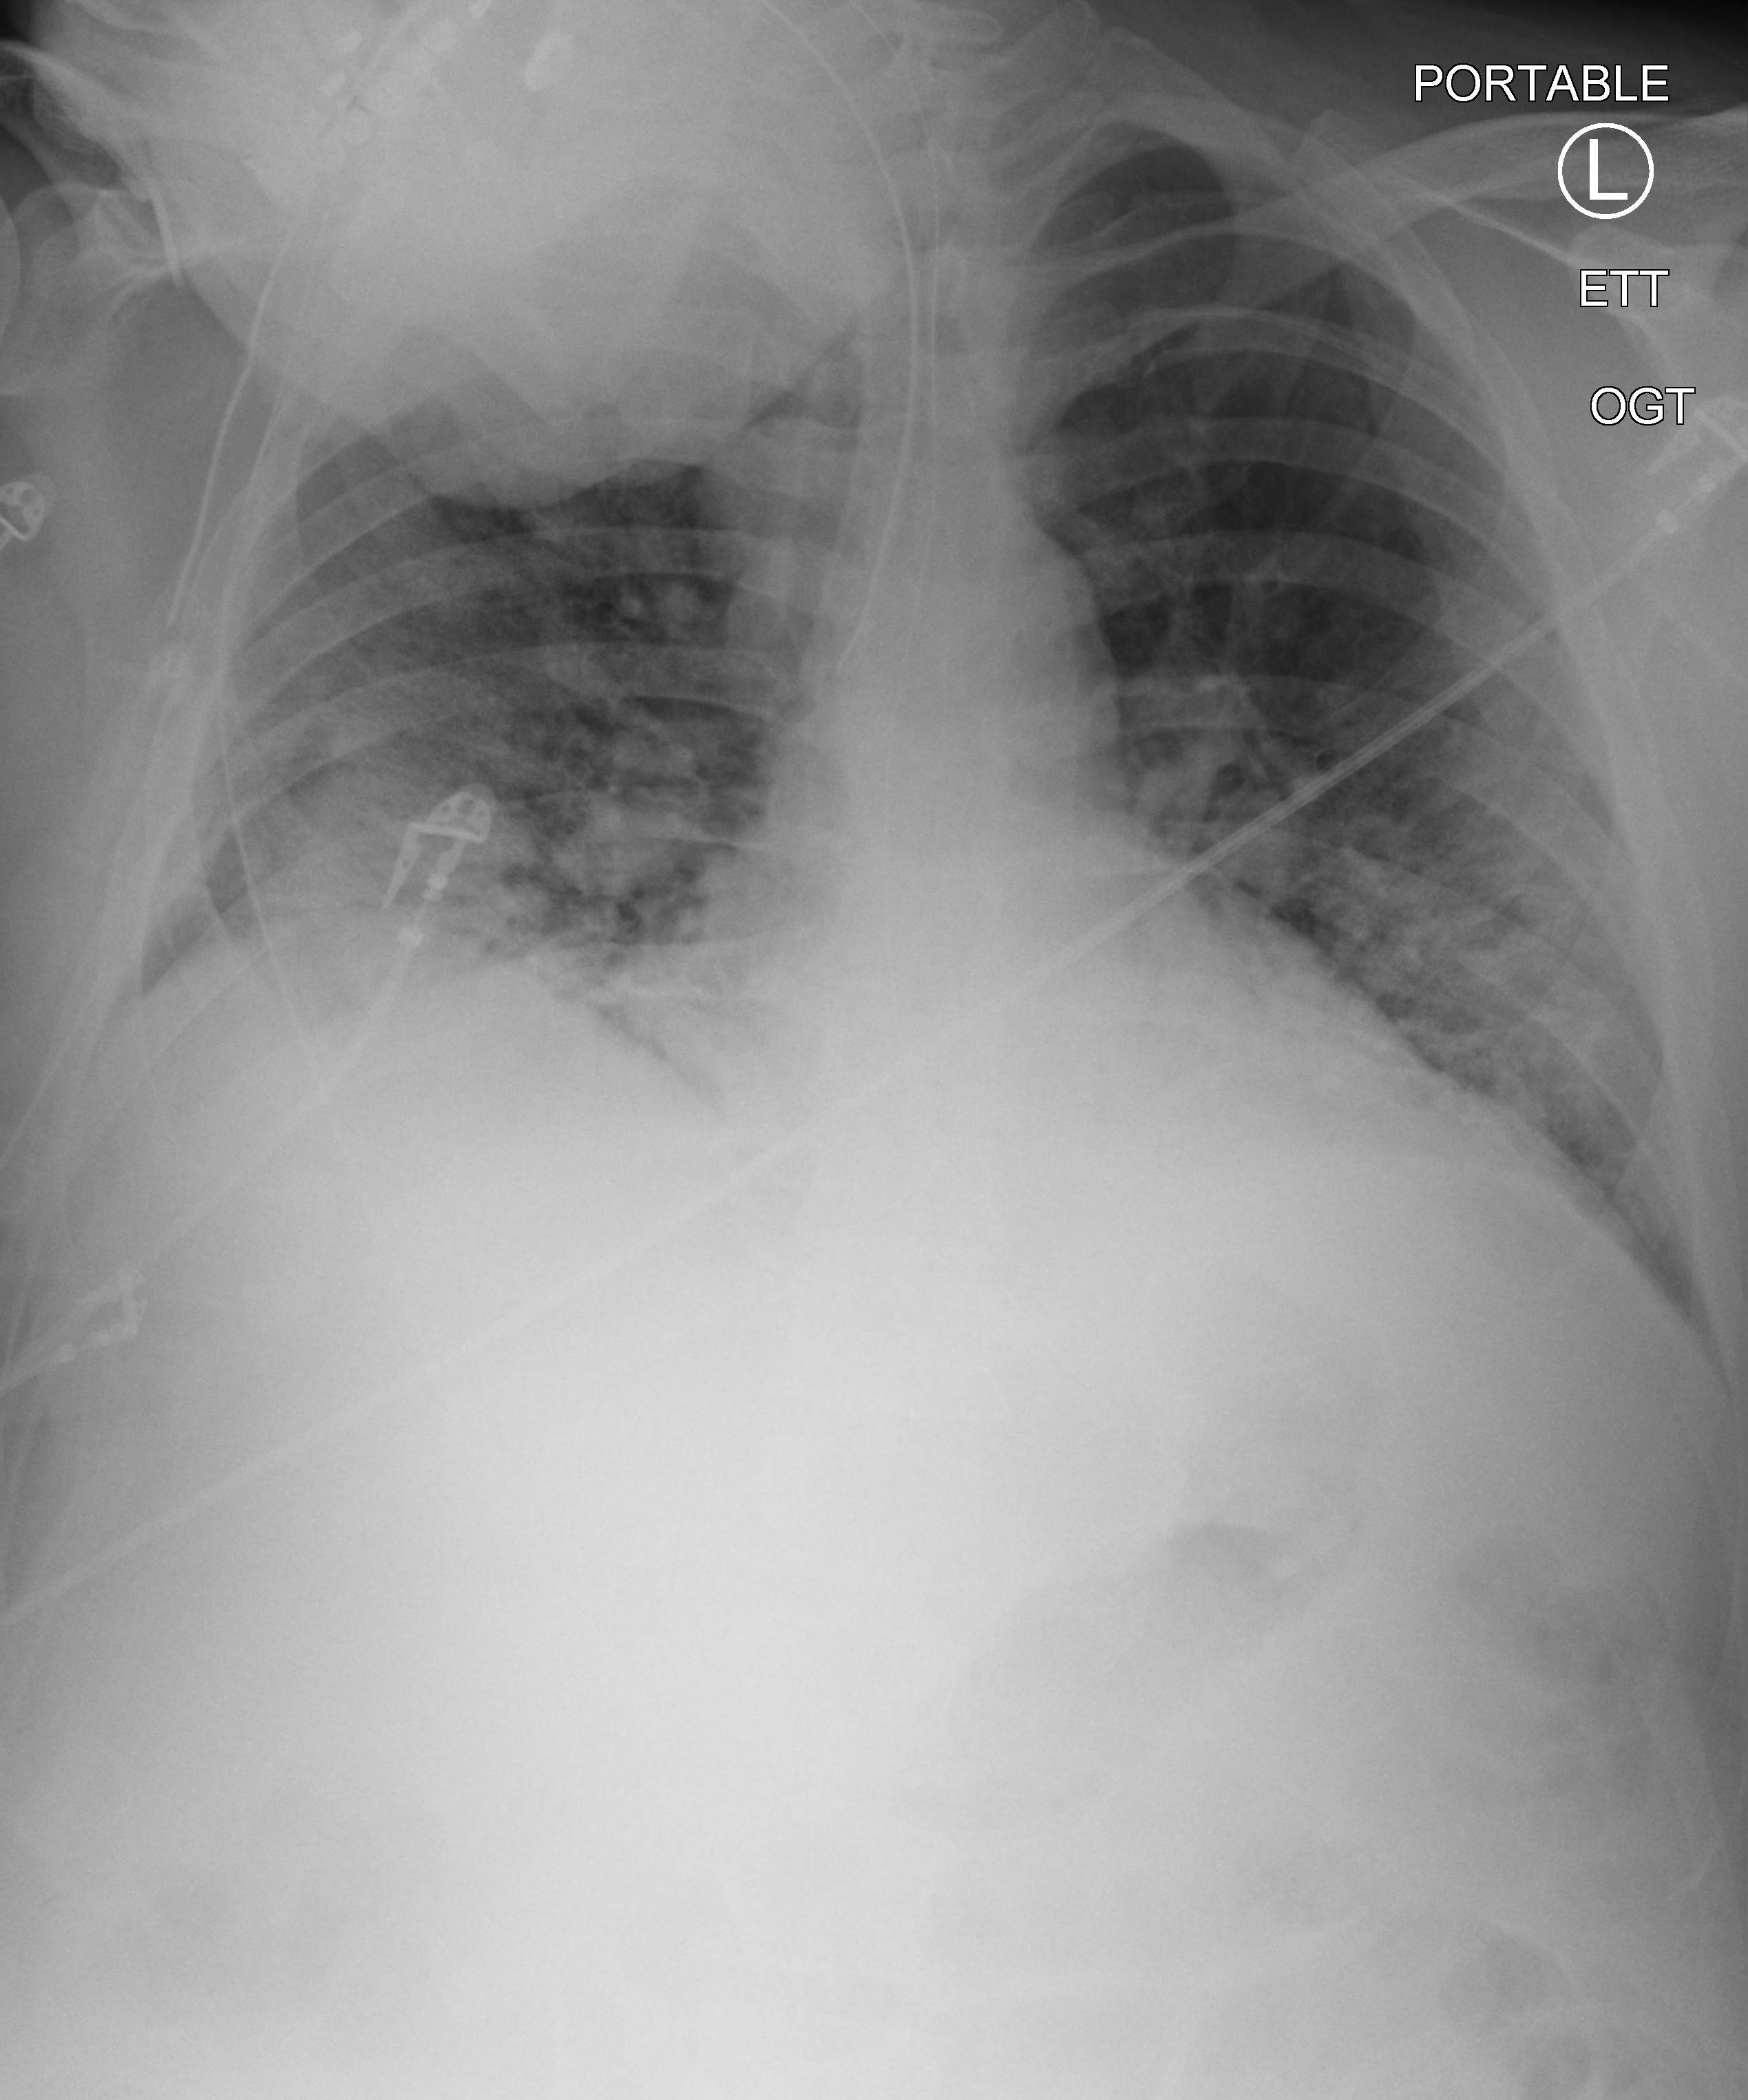
Bedside chest radiograph (computed radiography), anteroposterior (AP) projection. Male patient hospitalised with COVID-19, age 18–59 years.
Admission-level facts for this patient (not findings on this image; timing relative to this image not recorded): mechanically ventilated during this hospital stay: yes; admitted to intensive care during this hospital stay: yes; length of hospital stay: 80 days.